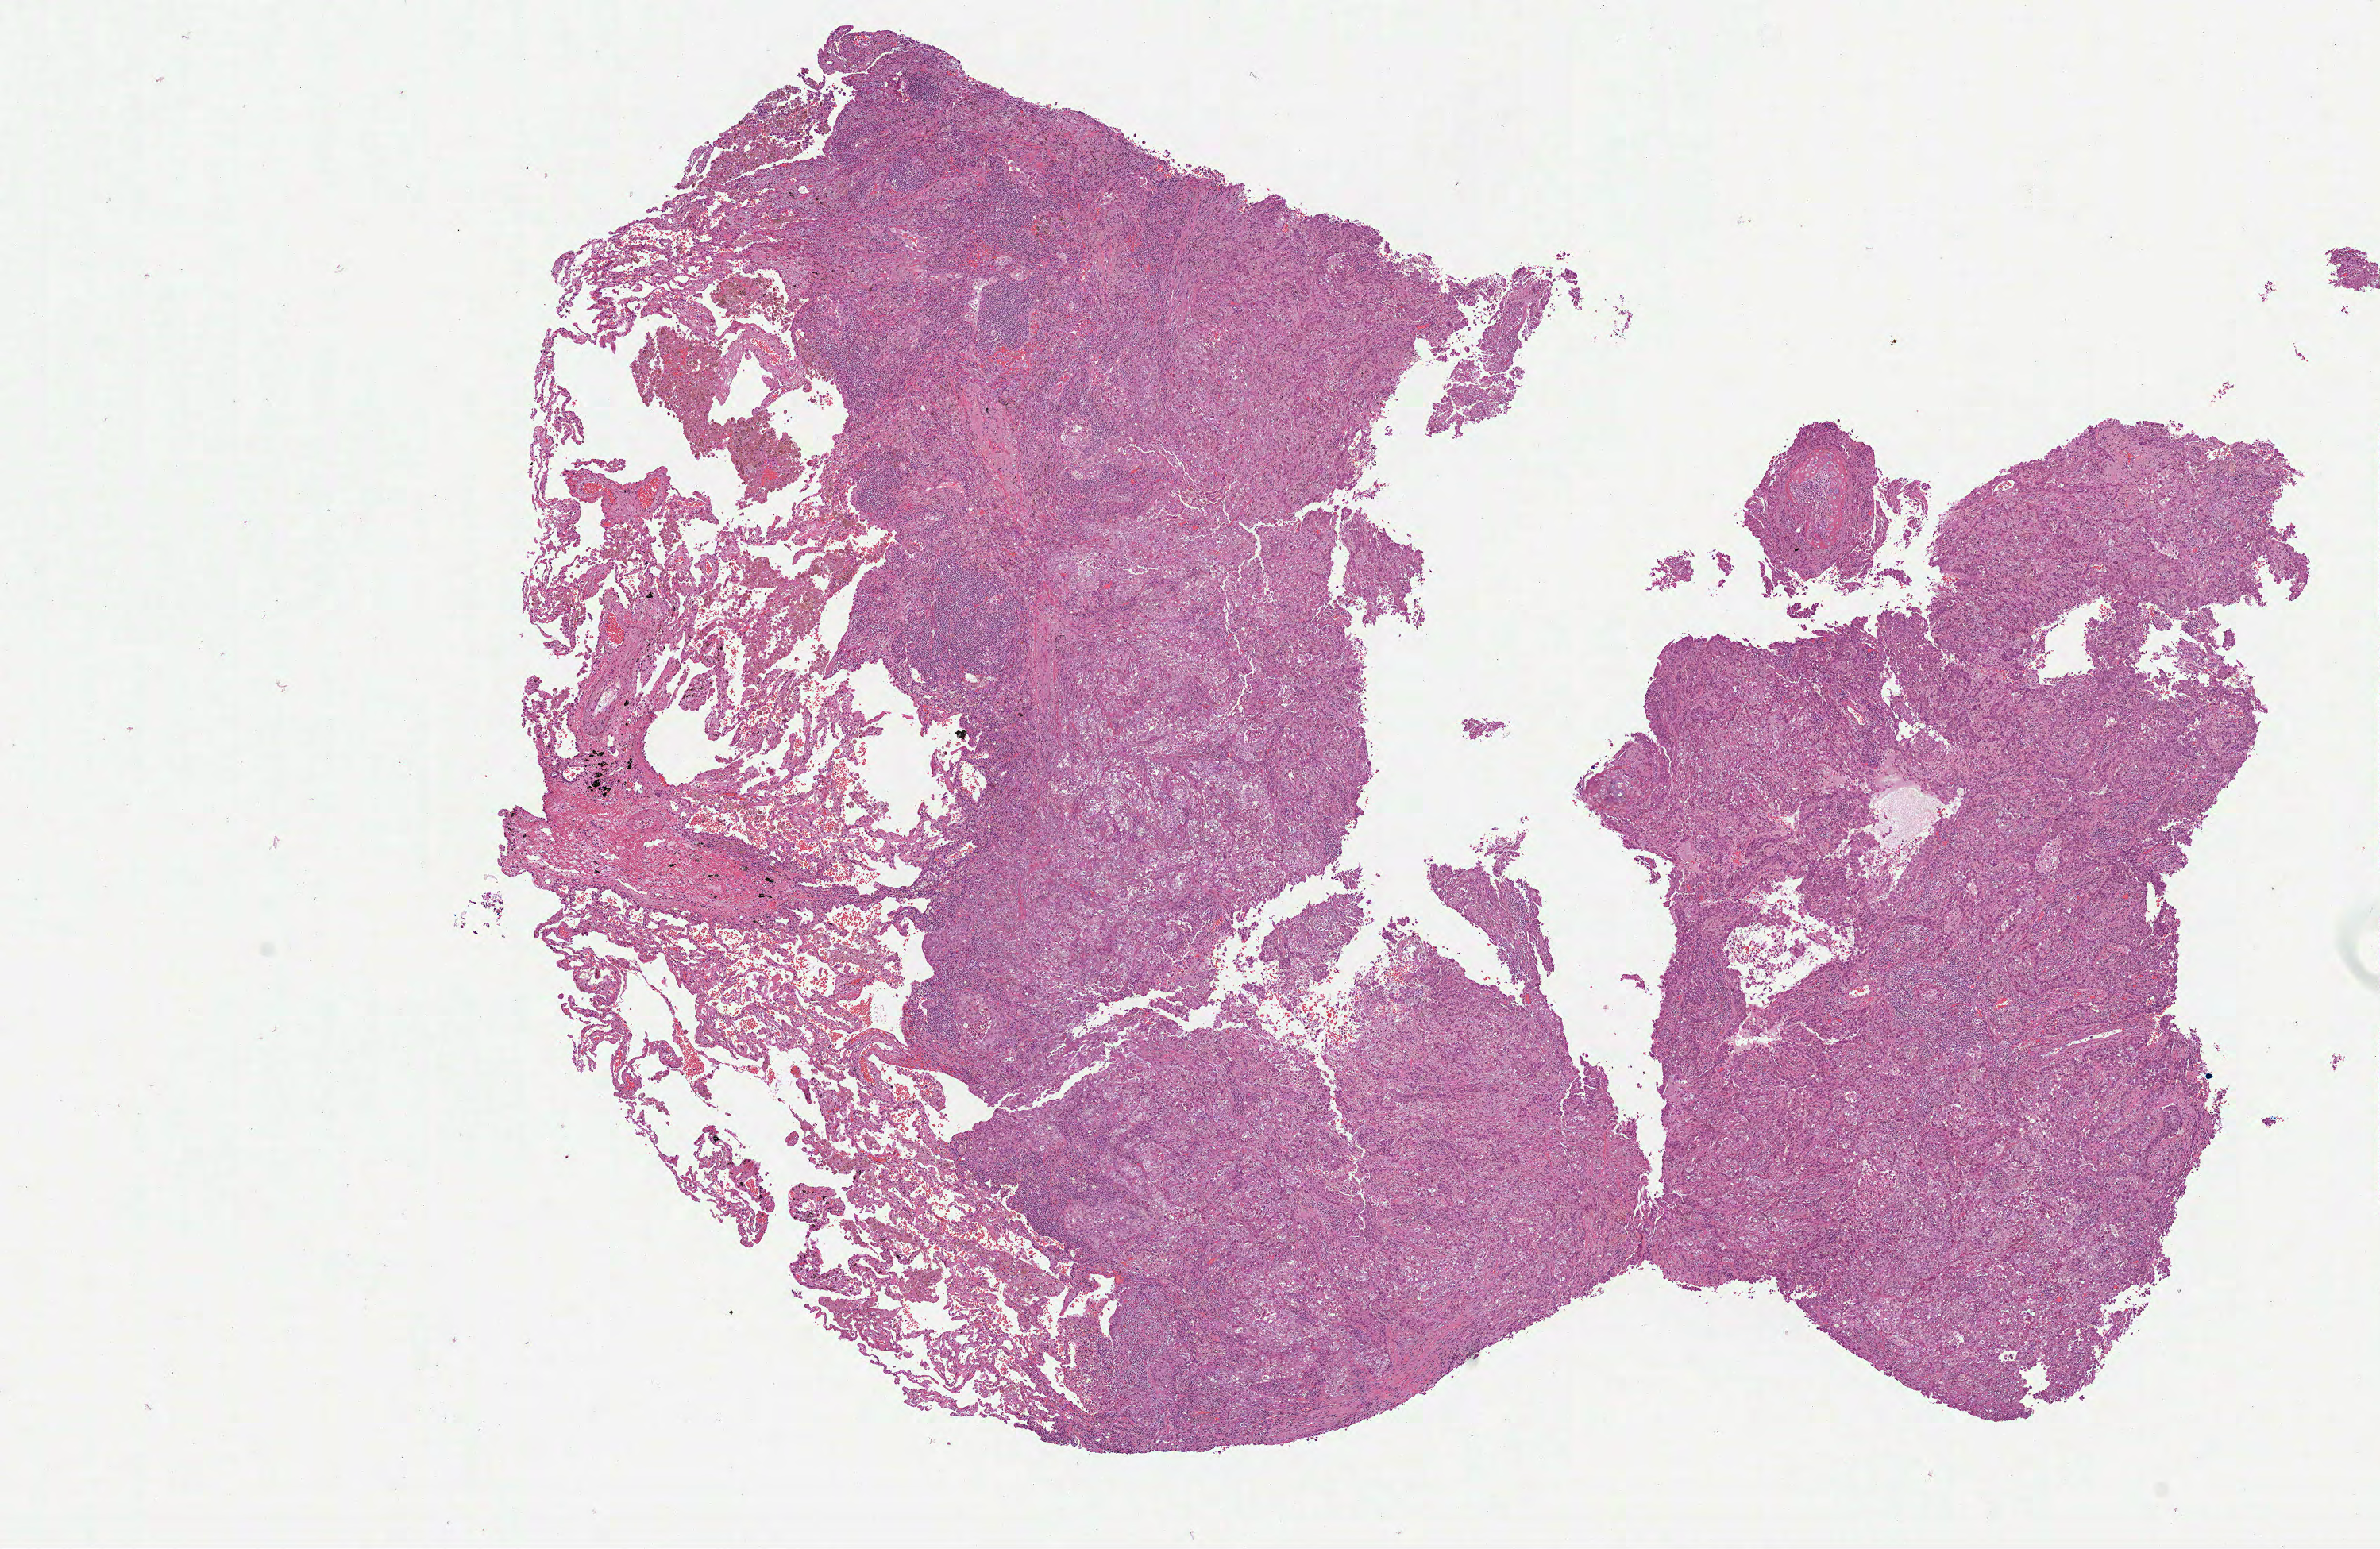
Whole-slide histology image, H&E — whole scanned area (about 12.1 x 7.9 mm) shown as a low-resolution overview, formalin-fixed paraffin-embedded (FFPE) diagnostic section, sample: primary tumour, lung. Female patient; age at initial diagnosis 73 years.
* pathologic diagnosis: Adenocarcinoma, NOS (upper lobe, lung)
* laterality: right
* AJCC pathologic stage: IB (7th edition)